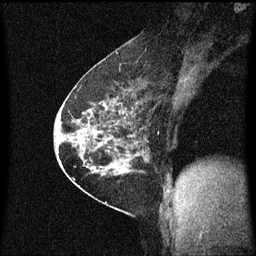
Breast MRI (dynamic contrast-enhanced), one sagittal slice. Slice 36 of 60 in the series (ordered by position). Dynamic contrast-enhanced series, image 2 of 3 at this slice position (ordered by acquisition). 1.5 T. TE 4.2 ms, TR 8.4 ms. 2 mm slice thickness. 256 × 256 image matrix, field of view 200 × 200 mm. Patient: female, 60 years.
Annotated regions visible in this slice (semi-automatically segmented with operator editing):
- analysis volume of interest (the breast-tissue region the enhancement analysis was run in; not a lesion): bounding box (x1, y1, x2, y2) in pixels: (69, 66, 150, 193)
- tumour enhancement mask (voxels above the 70 % enhancement threshold inside the analysis volume of interest): (69, 66, 148, 175)